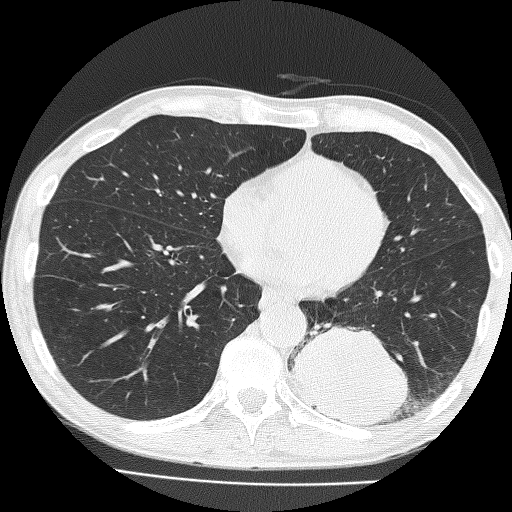
Chest CT (low-dose screening protocol), one axial image, first (baseline) screen, lung window (W 1500 / L -600 HU), 2 mm slice thickness. Male participant, aged 58 years at enrolment.
• Expert-annotated lung lesion, bounding box (x1, y1, x2, y2) in pixels: (296, 304, 424, 435).
• The screening reader recorded 2 non-calcified nodules or masses ≥4 mm on this exam; which of them this box marks is not recorded.
• Official screen result: positive, change unspecified: nodule(s) >= 4 mm or enlarging nodule(s), mass(es), or other non-specific abnormalities suspicious for lung cancer.
• Lung cancer was diagnosed 39 days after this screen: non-small cell carcinoma, left lower lobe, poorly differentiated (G3), stage IV (AJCC 6th edition), 74 mm at pathology.